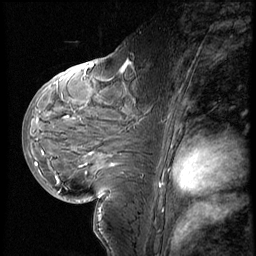
Breast MRI (dynamic contrast-enhanced), one sagittal slice. Position 31 of 60 along the scan axis. 3 images stored at this slice position (order not interpretable as contrast timing). 1.5 T. TE 4.2 ms, TR 8.9 ms. 256 × 256 image matrix, field of view 200 × 200 mm. Female patient, age 29 years. From the clinical record (not read from this slice): setting: breast cancer imaged before/during neoadjuvant chemotherapy.
Structures marked on this image (semi-automatic segmentation, software-assisted and operator-edited):
- analysis volume of interest (the breast-tissue region the enhancement analysis was run in; not a lesion): bounding box (x1, y1, x2, y2) in pixels: (29, 57, 152, 200)
- tumour enhancement mask (voxels above the 140 % enhancement threshold inside the analysis volume of interest): (37, 63, 130, 167)